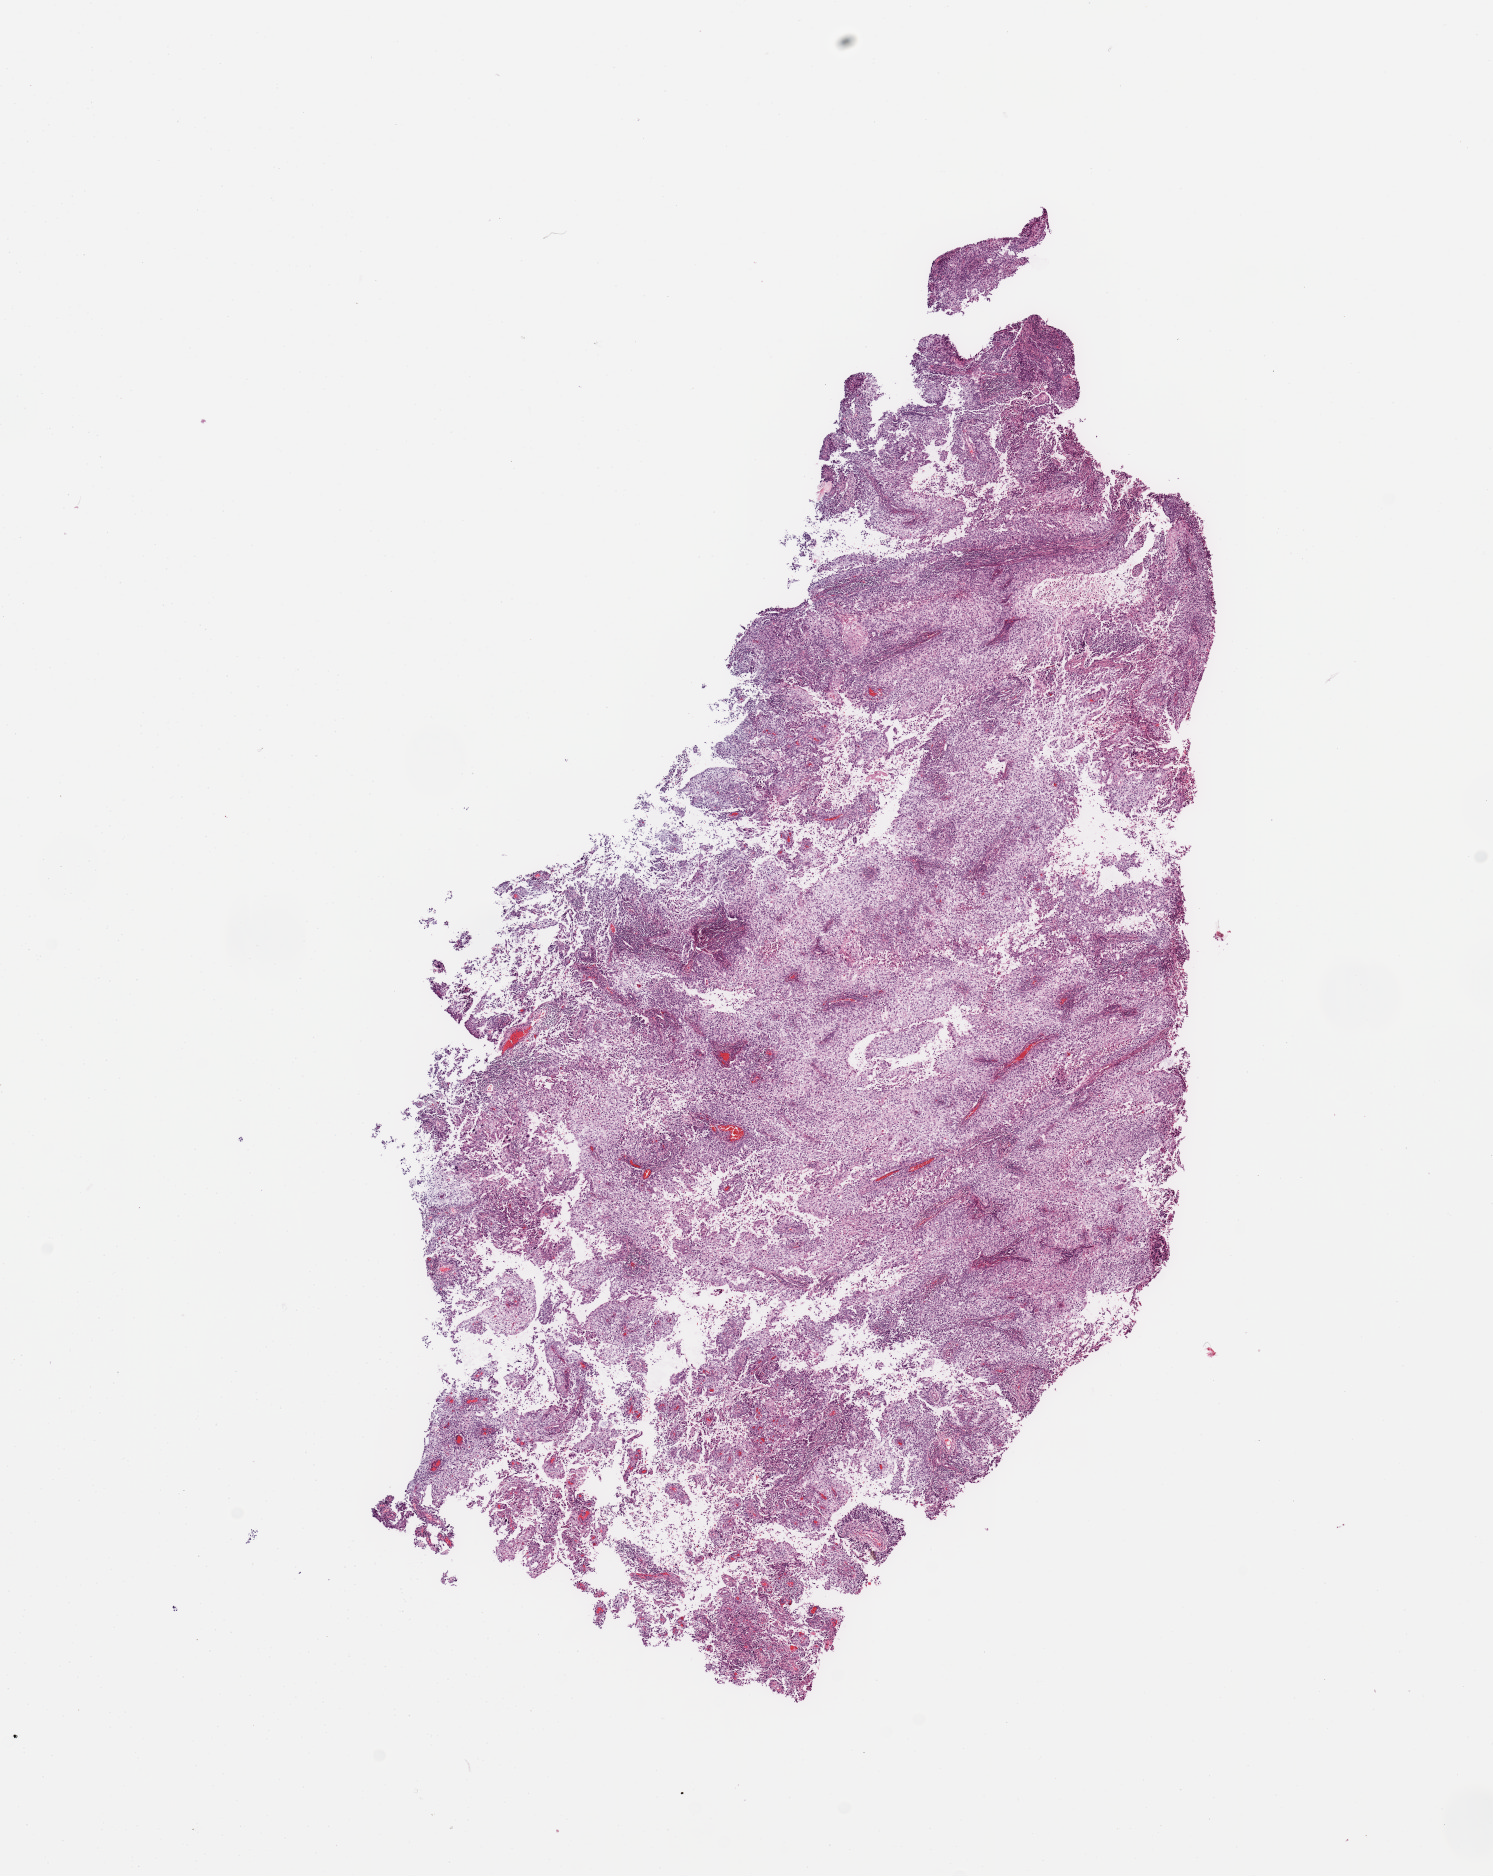
Digitized H&E-stained tissue section (whole slide), a low-resolution overview of the entire scanned area, about 11.8 x 14.8 mm, uterus, tumour tissue. 64-year-old female patient. Histologic grade: G3 (poorly differentiated).
Histologic diagnosis: Endometrioid adenocarcinoma, NOS. AJCC pathologic stage: III.